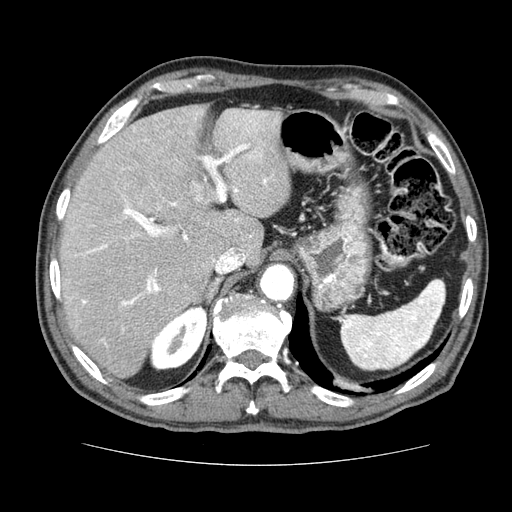
Contrast-enhanced abdominal CT (liver protocol), one axial slice; slice 51 of 79 in the series (ordered by position); 120 kVp; soft-tissue window (W 400 / L 40 HU); 2.5 mm slice thickness; 512 × 512 image matrix, field of view 360 × 360 mm. From the clinical record (not read from this slice): diagnosis: hepatocellular carcinoma (patient treated with transarterial chemoembolisation; whether this scan precedes or follows treatment is not stated here); TNM stage (as recorded): Stage-I; Child-Pugh class: A.
Outlined on this slice (semi-automatic segmentation, software-assisted and operator-edited):
- liver parenchyma outside the tumour (the mass and vessels are separate outlines, so this box may not span the whole liver): bounding box (x1, y1, x2, y2) in pixels: (60, 104, 290, 378)
- liver vessels: (70, 111, 277, 345)